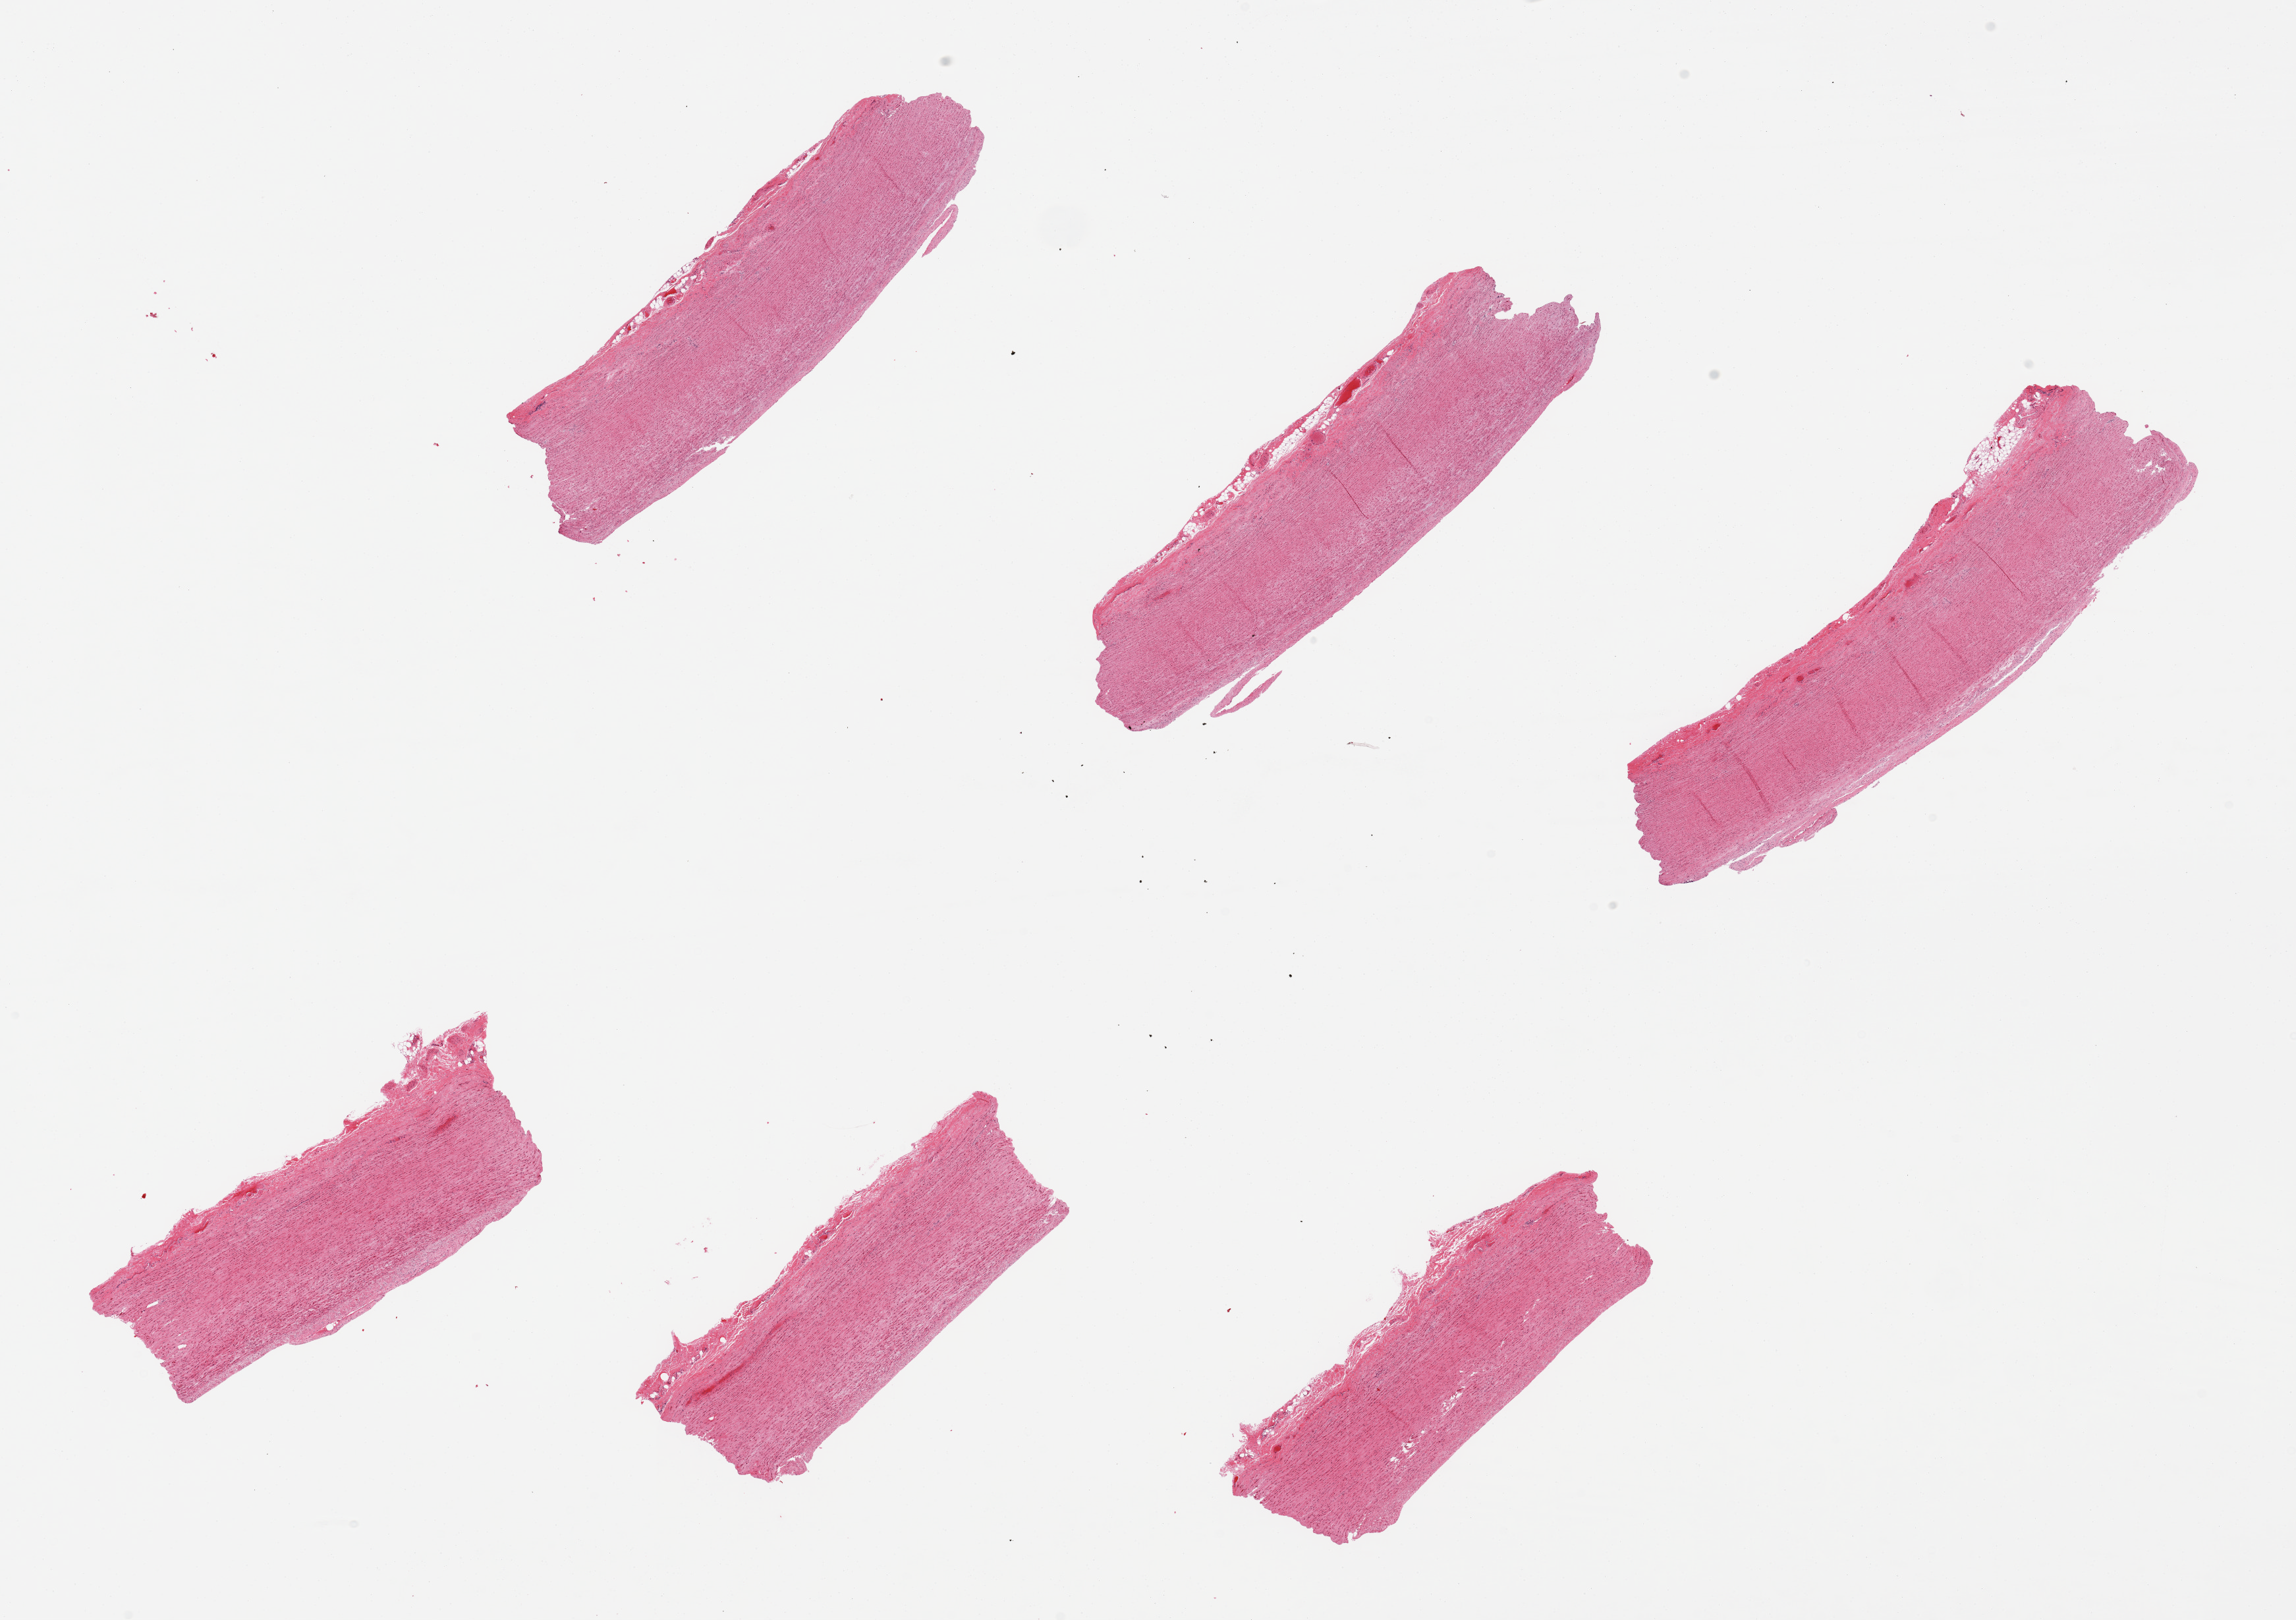
Hematoxylin and eosin (H&E) whole-slide image, low-resolution overview of the scanned area, about 27.6 x 19.4 mm (acquisition: 20x scan). PAXgene-fixed paraffin-embedded (PFPE) section. Sampled site (target tissue): aorta. Tissue donor sample. Donor sex: male.
• review note (as recorded): 6 pieces, intimal thickening